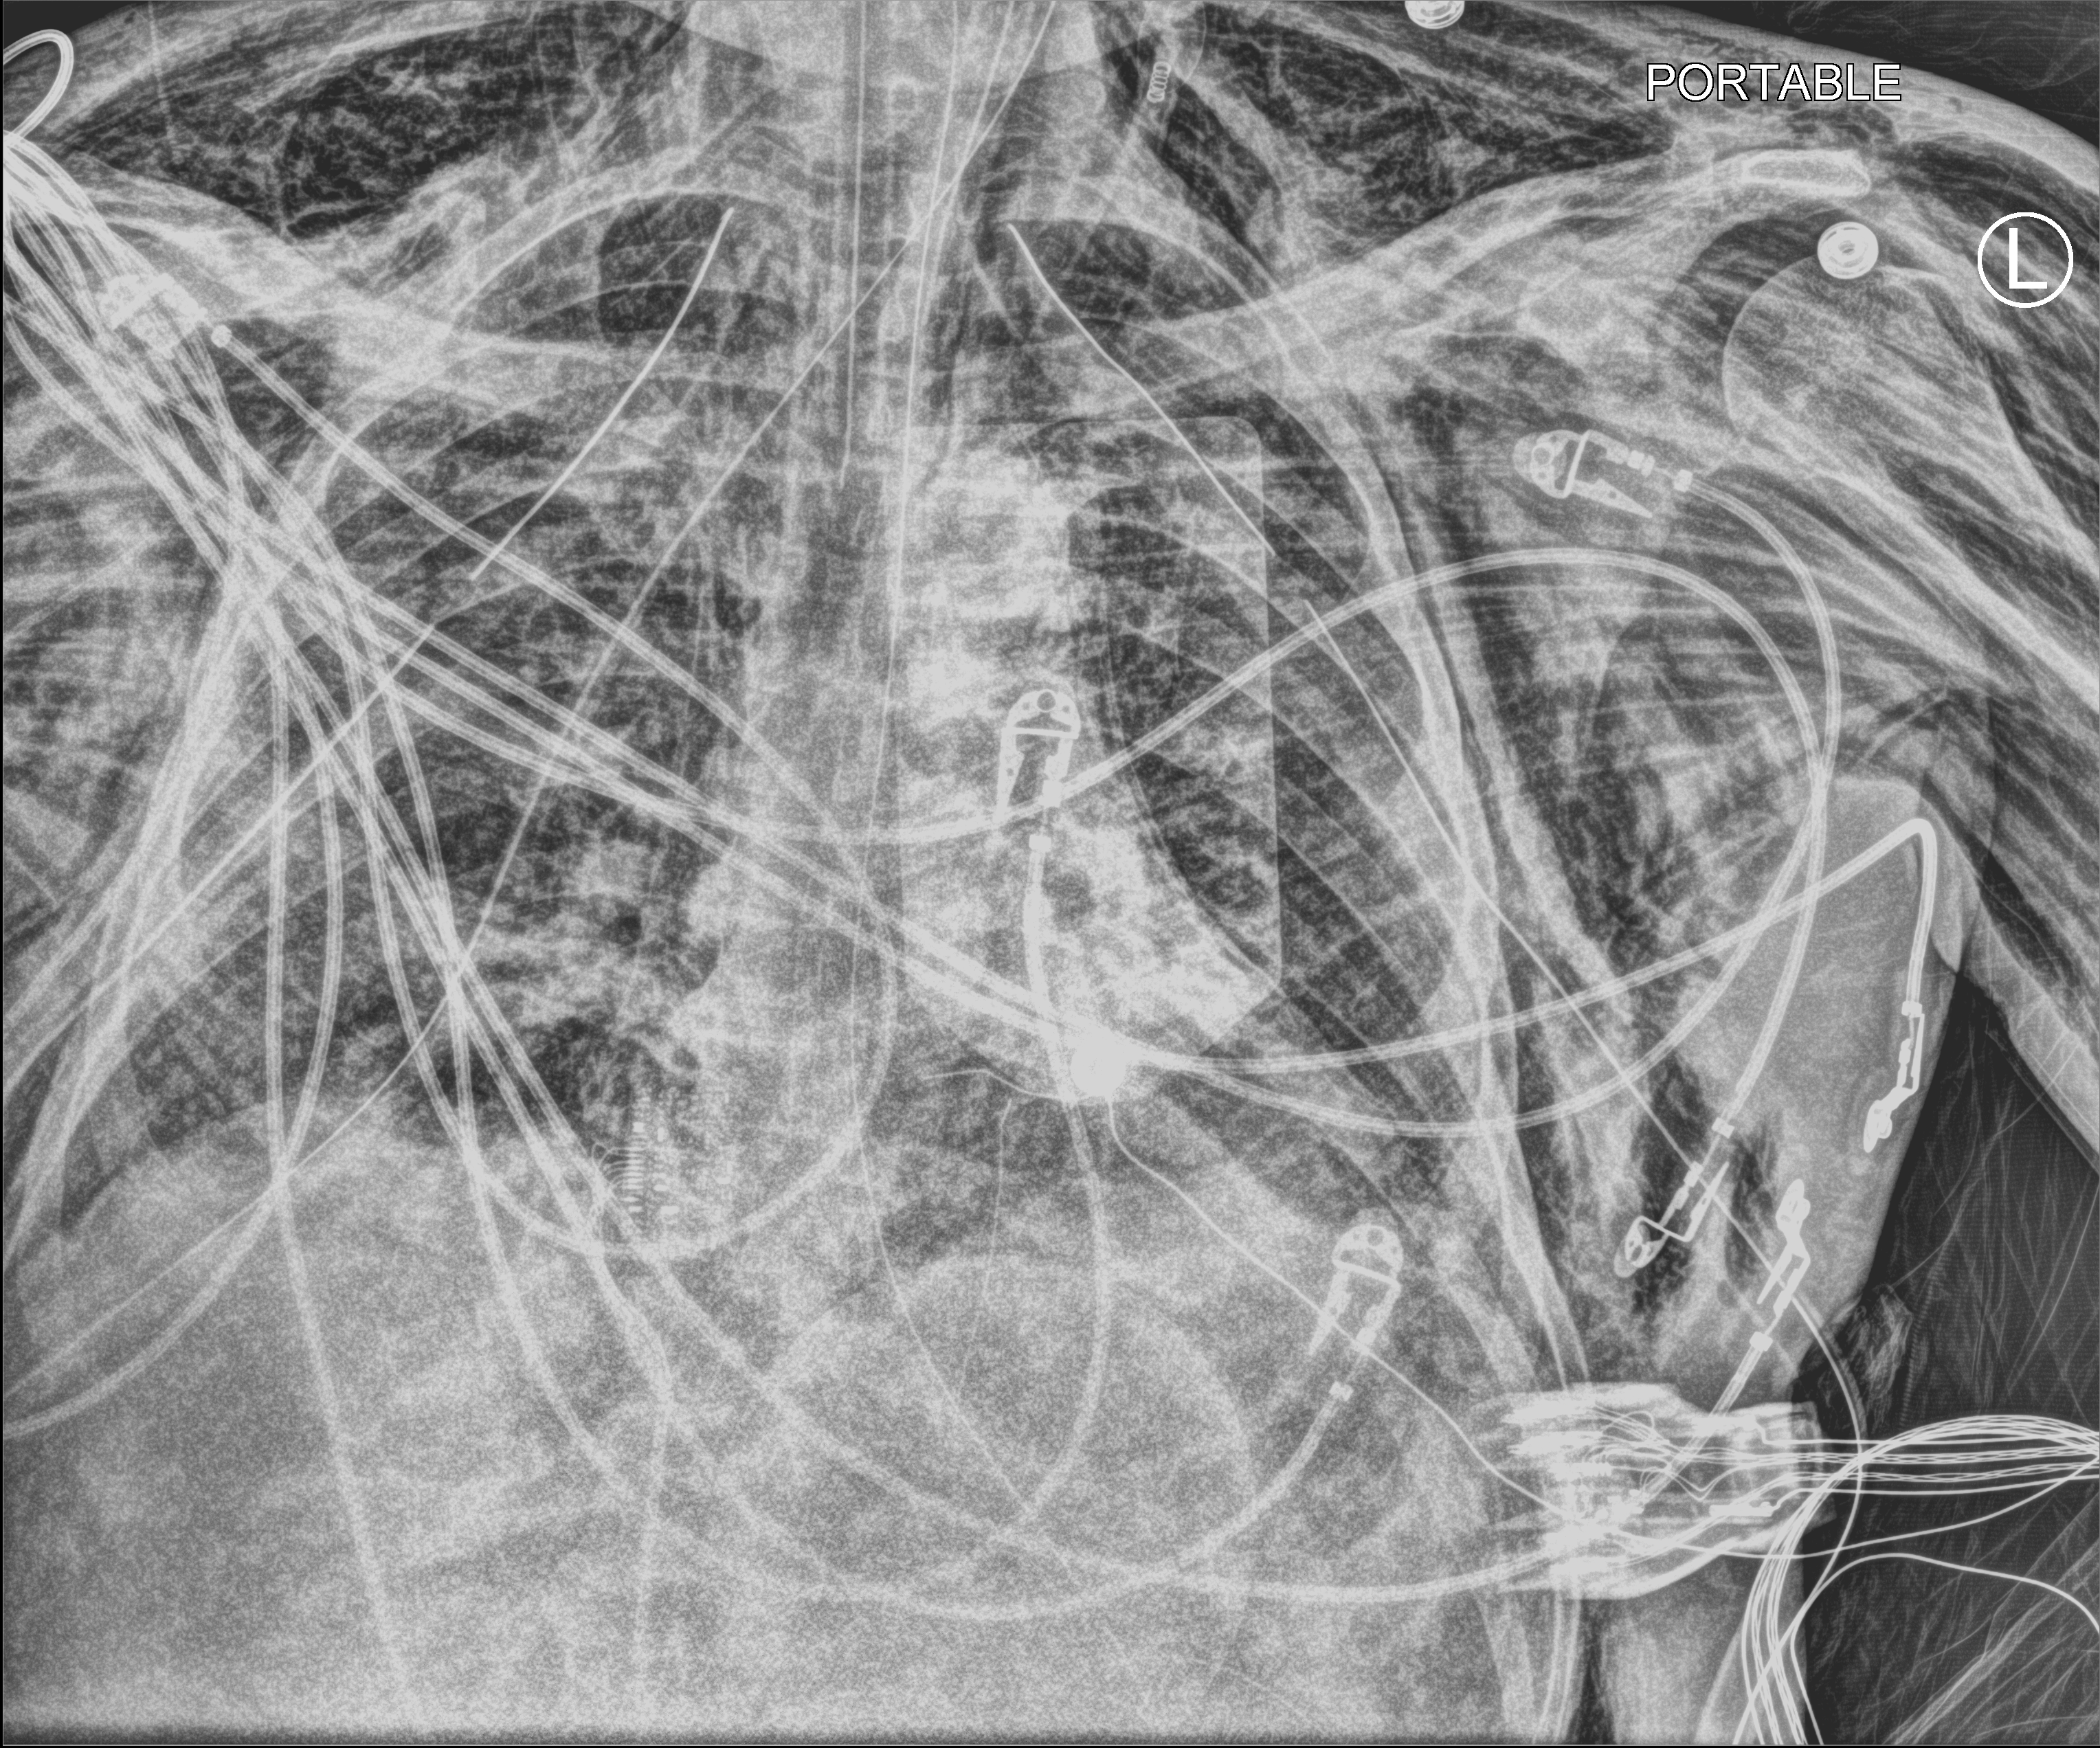
Portable chest radiograph; anteroposterior (AP) projection. Male patient hospitalised with COVID-19, age 18–59 years.
From the hospital-stay record, not from the radiograph (when in the stay this image was taken is not recorded): COPD (admission record): no; mechanically ventilated during this hospital stay: yes.